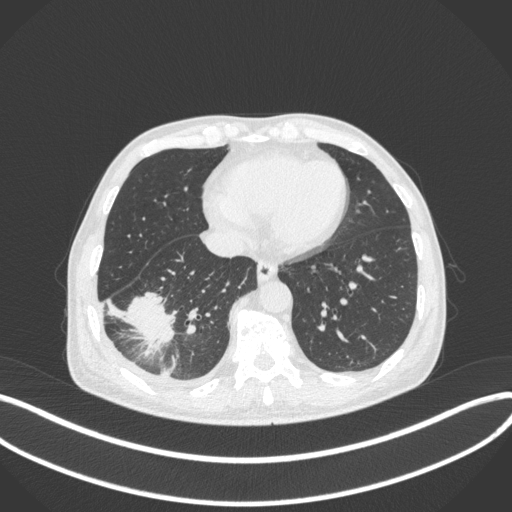
Chest CT, one axial slice. Slice 115 of 385 in the series (ordered by position). Reconstruction kernel B31f. 120 kVp. Lung window (W 1500 / L -600 HU). 1 mm slice thickness. 512 × 512 image matrix, field of view 400 × 400 mm. Male patient, age 64 years. From the clinical record (not read from this slice): clinical TNM (as recorded): T3 N0 M0.
Structures marked on this image (rectangle marked by the reading radiologist):
- lung tumour (recorded histology: adenocarcinoma): box from (x=124, y=285) to (x=179, y=359) px